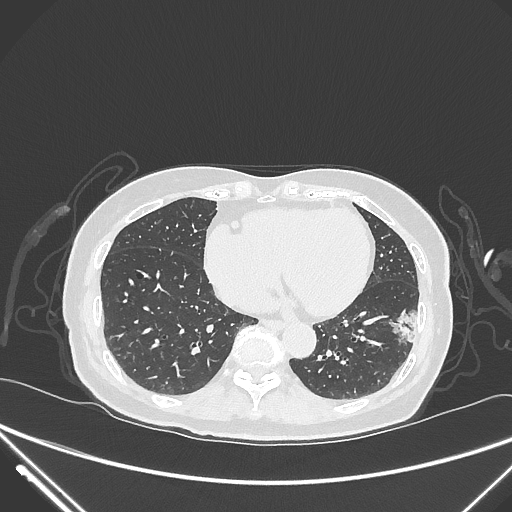
Chest CT, one axial slice. Position 107 of 310 along the scan axis. 120 kVp. Lung window (W 1500 / L -600 HU). 1 mm slice thickness. 512 × 512 image matrix. Female patient, age 82 years. From the clinical record (not read from this slice): clinical TNM (as recorded): T1c N0 M0; histopathological grade: G2.
Annotated regions visible in this slice (rectangle marked by the reading radiologist):
- lung tumour (recorded histology: adenocarcinoma): box from (x=387, y=304) to (x=425, y=350) px